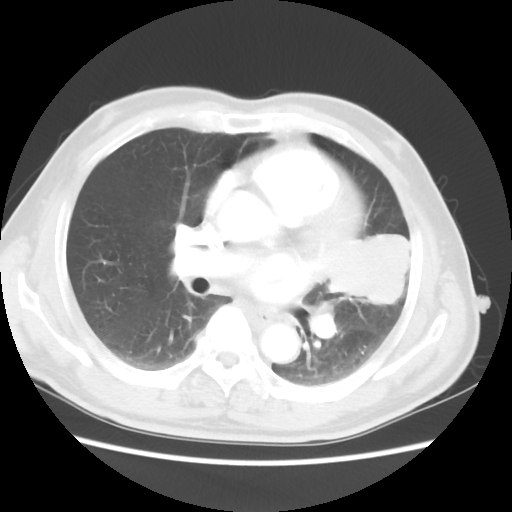
Chest CT, one axial slice. Position 26 of 50 along the scan axis. Lung window (W 1500 / L -600 HU). 5 mm slice thickness. 512 × 512 image matrix, field of view 360 × 360 mm. Male patient, age 69 years. Case-level facts recorded for this patient, not image findings: clinical TNM (as recorded): T3 N1 M1a.
Outlined on this slice (bounding box drawn by a radiologist):
- lung tumour (recorded histology: squamous cell carcinoma): bounding box [x1, y1, x2, y2] px = [327, 224, 413, 316]